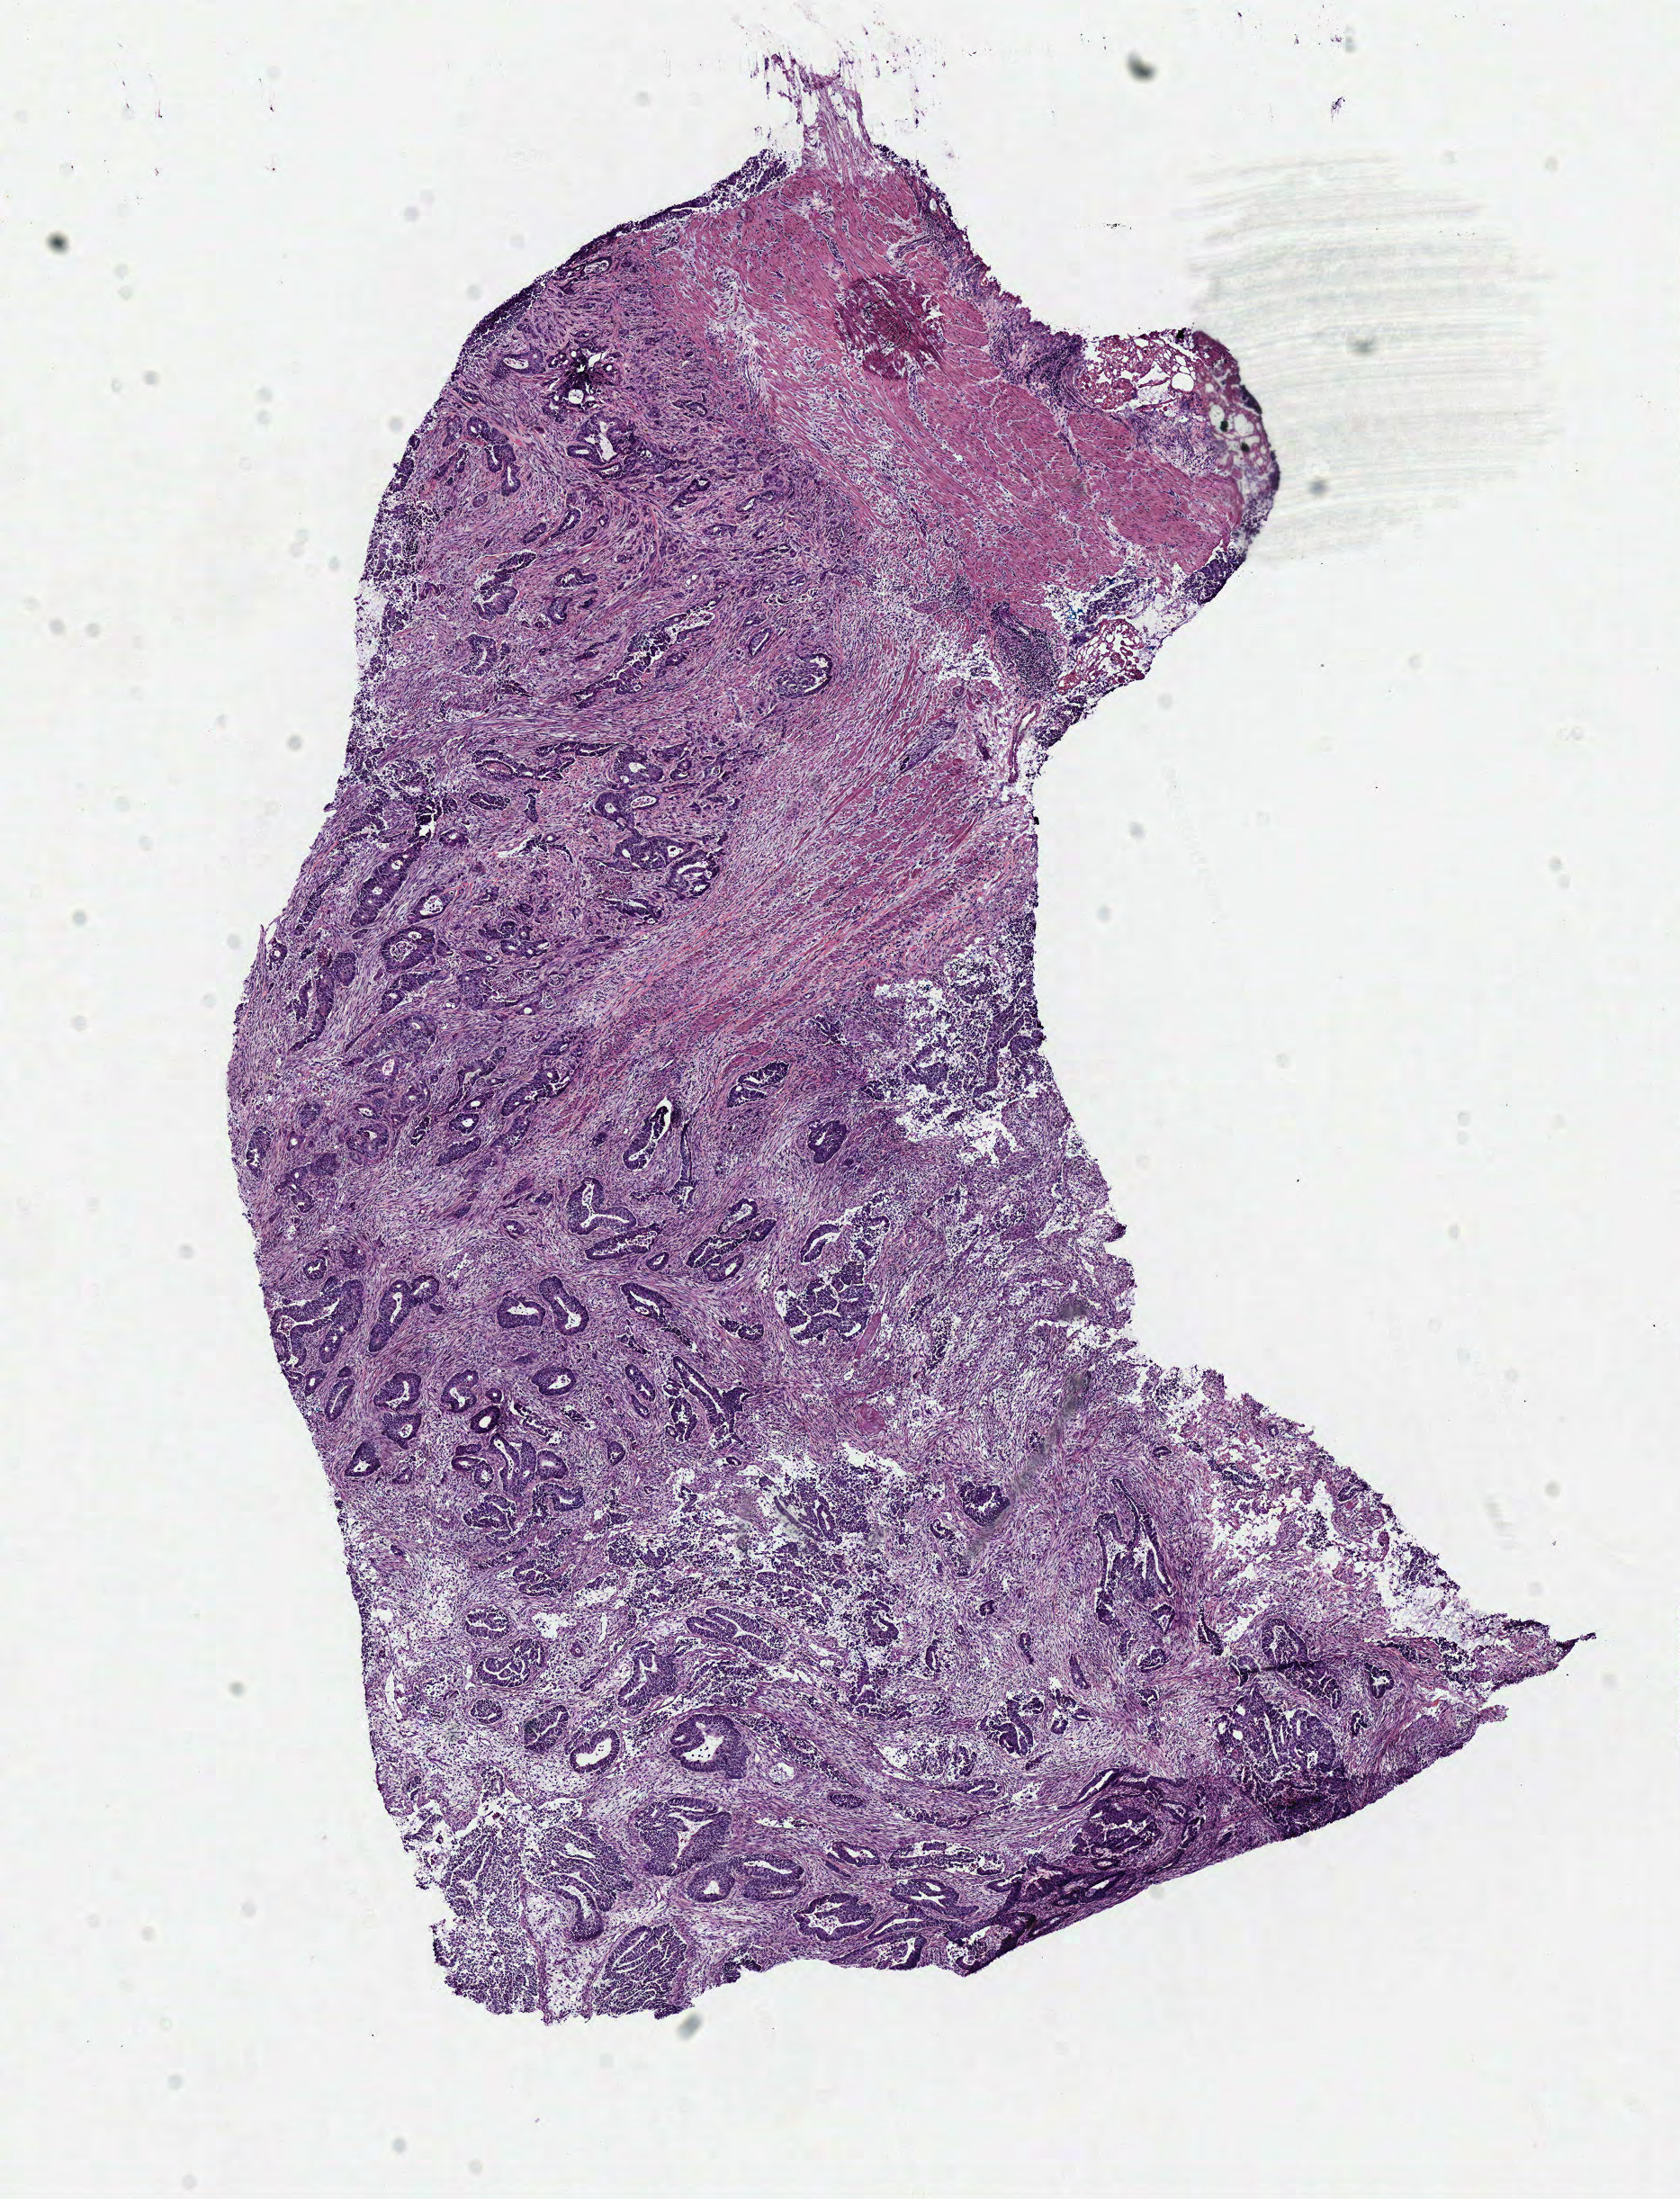
Whole-slide histology image, H&E — shown as a low-resolution overview of the whole scanned area (about 7.3 x 9.6 mm); frozen section from the top of the tissue portion; sample: primary tumour, colon. Patient: female, age at initial diagnosis 76 years. Composition of this section per pathologist review: tumour cells 70%, tumour nuclei 70%, normal cells 0%, stromal cells 25%, necrosis 5%.
Diagnosis: Adenocarcinoma, NOS (cecum). TNM: T3 N2 M1. AJCC pathologic stage: IV (6th edition).